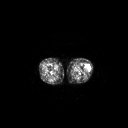
FDG PET of an extremity soft-tissue mass (from a PET/CT study), one axial slice. Position 181 of 223 along the scan axis. 3.27 mm slice thickness. 128 × 128 image matrix, field of view 700 × 700 mm. Female patient, age 16 years. From the clinical record (not read from this slice): histological type: spindle cell suggestive of biphasic synovial sarcoma; grade: intermediate; site of the primary tumour: left knee.
Annotated regions visible in this slice (expert contour drawn on MRI and transferred to this co-registered scan by the dataset authors):
- gross tumour volume including surrounding oedema: bounding box [x1, y1, x2, y2] px = [86, 63, 91, 70]
- gross tumour volume (mass): [86, 63, 91, 70]